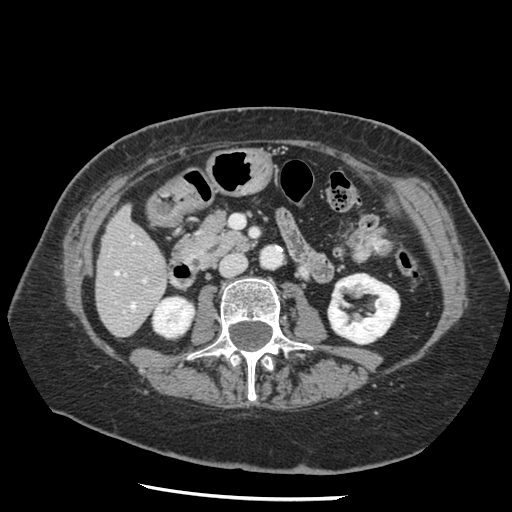
Contrast-enhanced abdominal CT, one axial slice. Slice 44 of 148 in the series (ordered by position). Reconstruction kernel STANDARD. 120 kVp. Intravenous contrast given. Soft-tissue window (W 400 / L 40 HU). 512 × 512 image matrix. Female patient, age 85 years. Case-level facts recorded for this patient, not image findings: diagnosis: colorectal cancer liver metastases, imaged before liver resection.
Outlined on this slice (expert manual segmentation):
- hepatic veins: box from (x=115, y=271) to (x=135, y=309) px
- liver: (x=96, y=208)–(x=168, y=336)
- planned liver remnant (the part of the liver to remain after resection): (x=96, y=208)–(x=168, y=331)